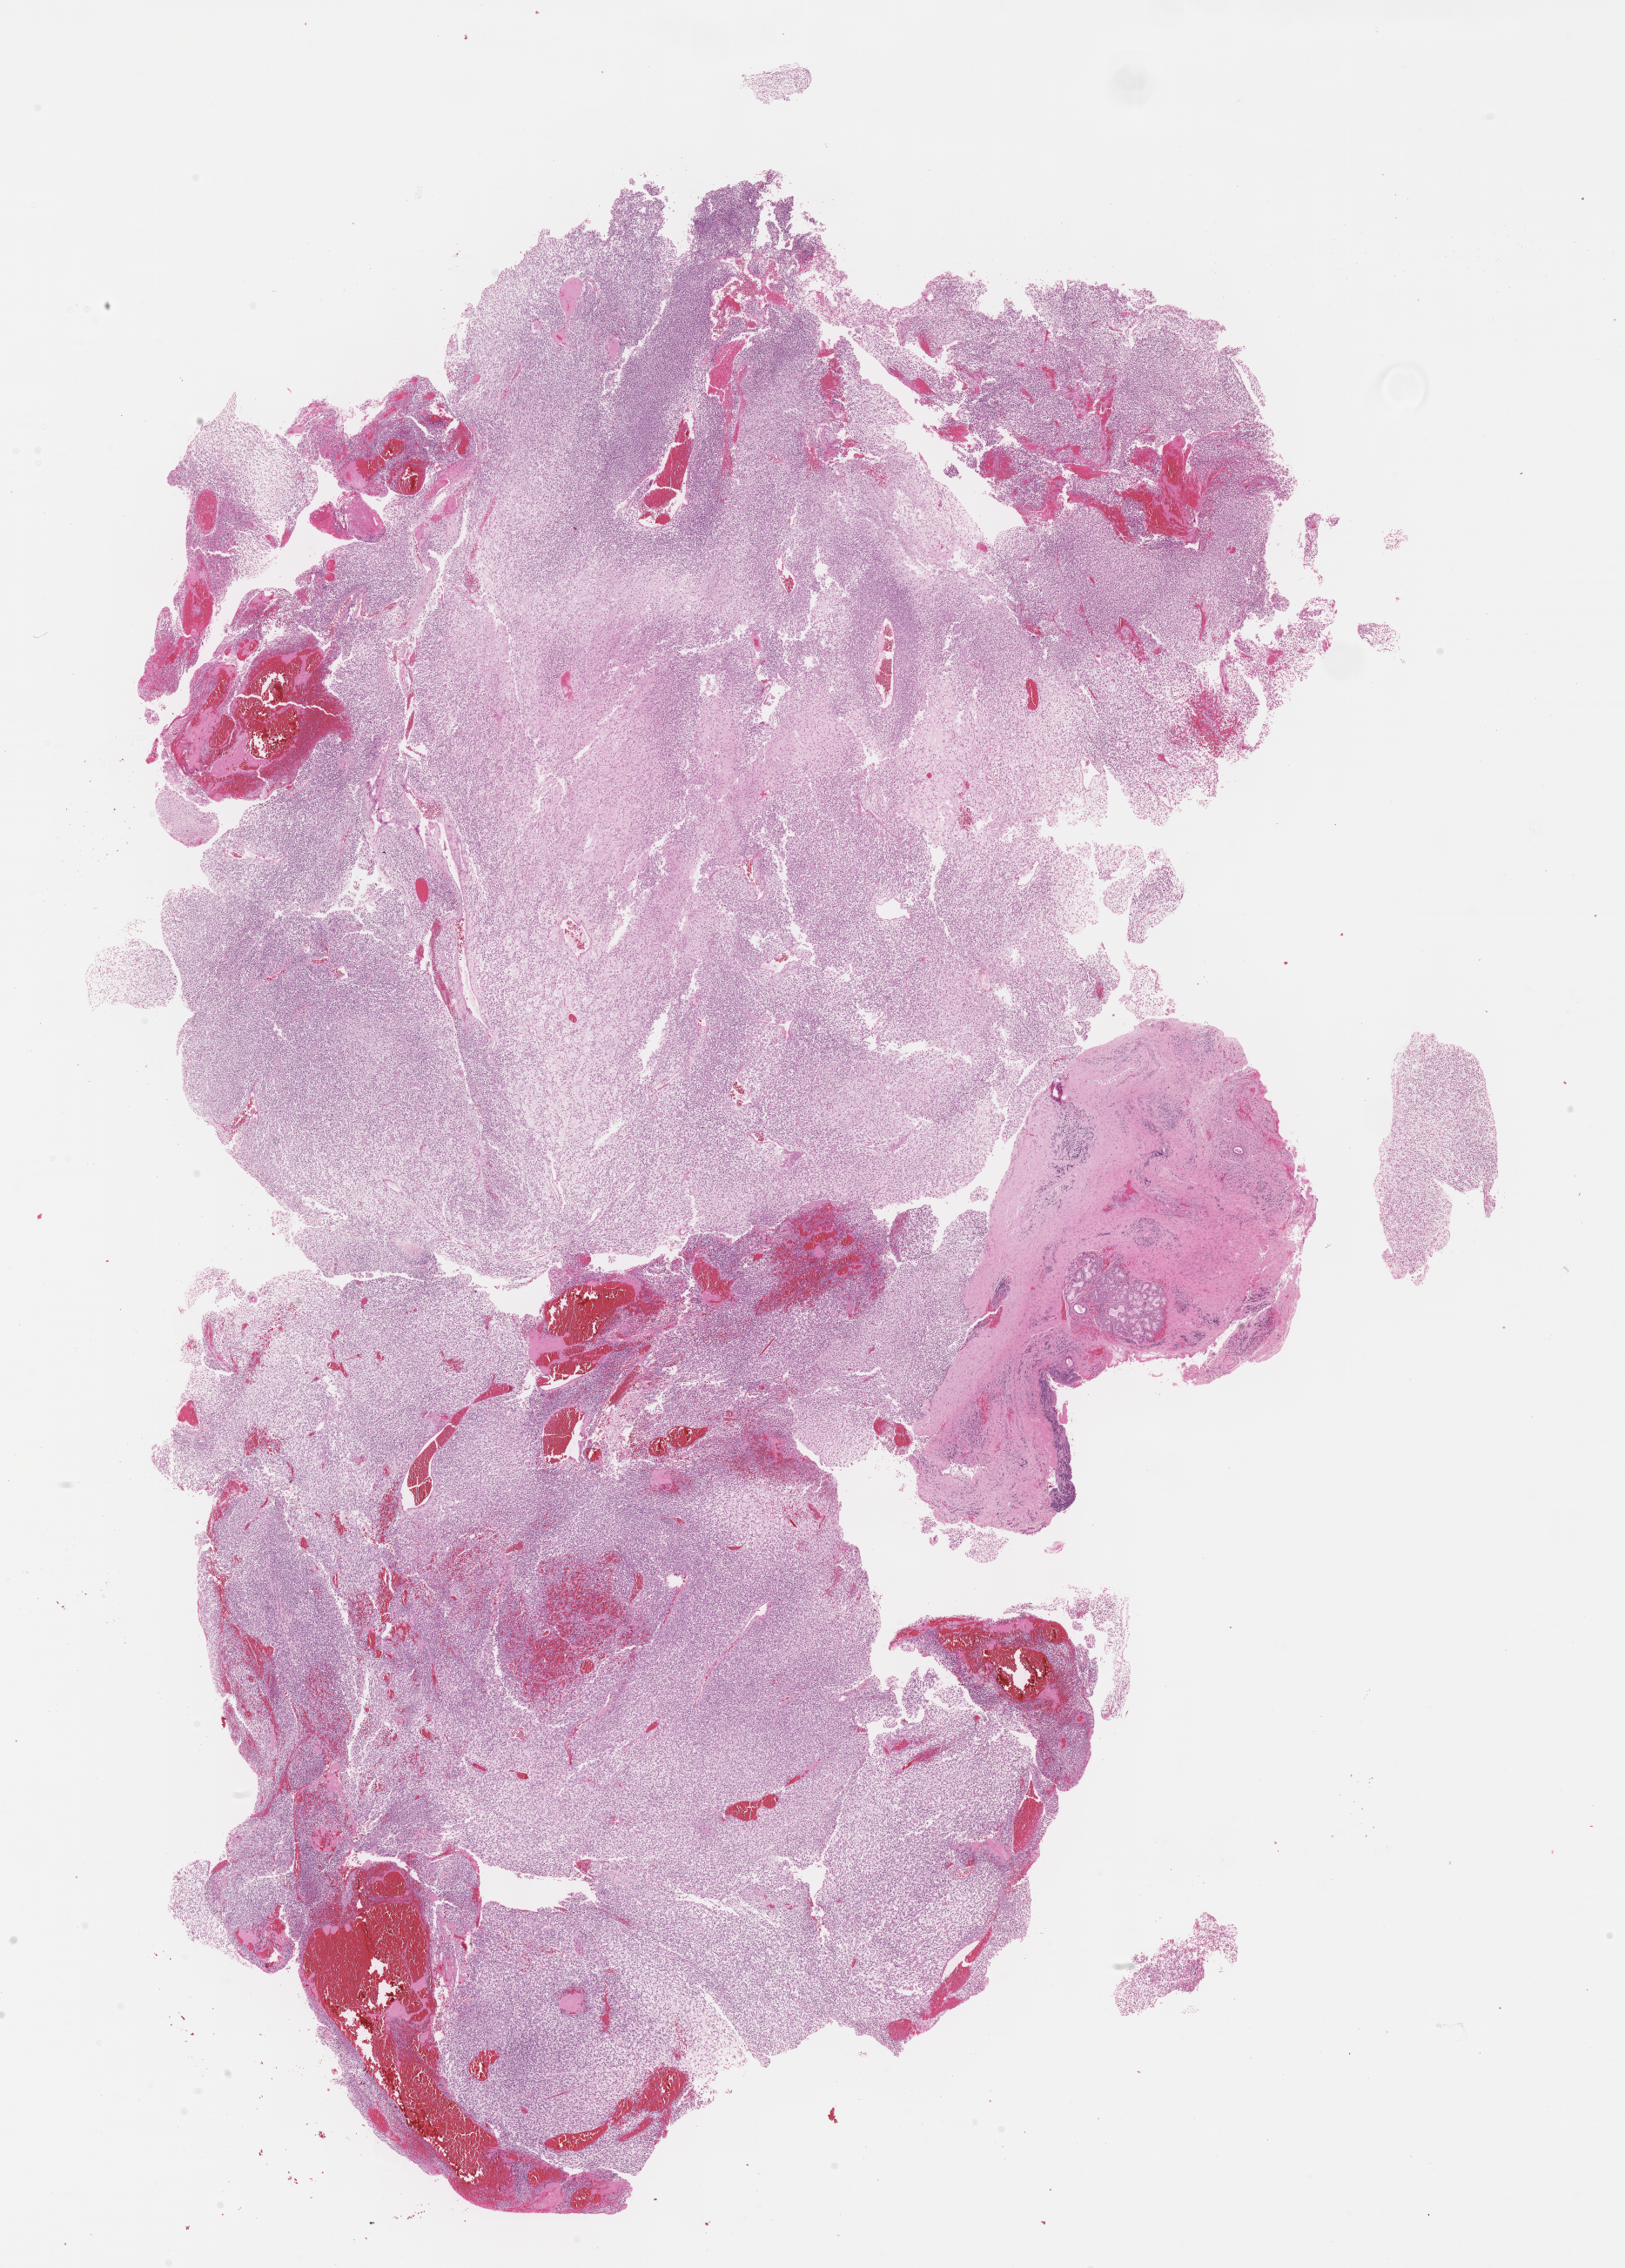
Digitized haematoxylin and eosin-stained section of tumor tissue — low-resolution overview of the scanned area, about 15.1 x 21.1 mm; formalin-fixed, paraffin-embedded (FFPE) tissue; site: nasopharynx-left. Male patient, age at diagnosis 11.1 years.
Diagnosis: rhabdomyosarcoma; histological classification: embryonal rhabdomyosarcoma.